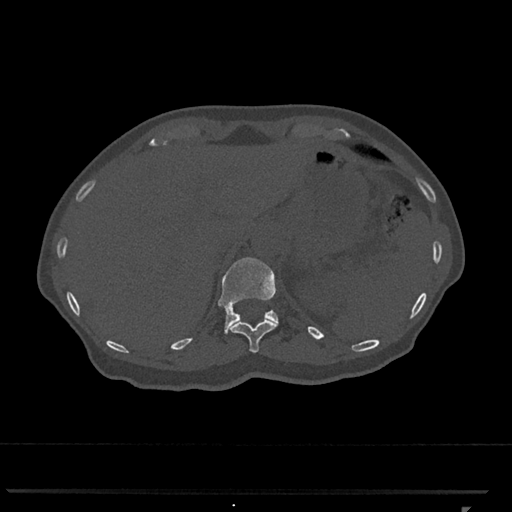
CT including the spine, one axial slice. Position 492 of 793 along the scan axis. 120 kVp. Bone window (W 1800 / L 400 HU). 512 × 512 image matrix. Female patient, age 62 years. From the clinical record (not read from this slice): primary cancer: renal.
Annotated regions visible in this slice (semi-automatically segmented with operator editing):
- T11 vertebra: bounding box [x1, y1, x2, y2] px = [230, 319, 278, 353]
- T12 vertebra: [218, 257, 278, 334]